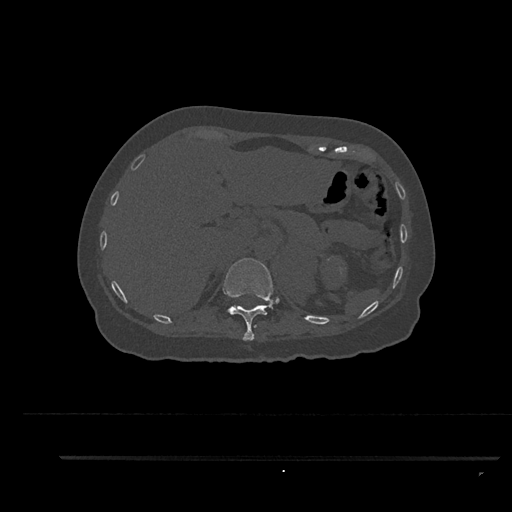
CT including the spine, one axial slice. Slice 309 of 797 in the series (ordered by position). Bone window (W 1800 / L 400 HU). 0.5 mm slice thickness. 512 × 512 image matrix, field of view 408 × 408 mm. Female patient, age 44 years. From the clinical record (not read from this slice): primary cancer: renal; vertebrae with lytic lesions (as recorded): L1.
Annotated regions visible in this slice (semi-automatic segmentation, software-assisted and operator-edited):
- T11 vertebra: bounding box (x1, y1, x2, y2) in pixels: (223, 258, 273, 341)
- T12 vertebra: (227, 308, 230, 312)